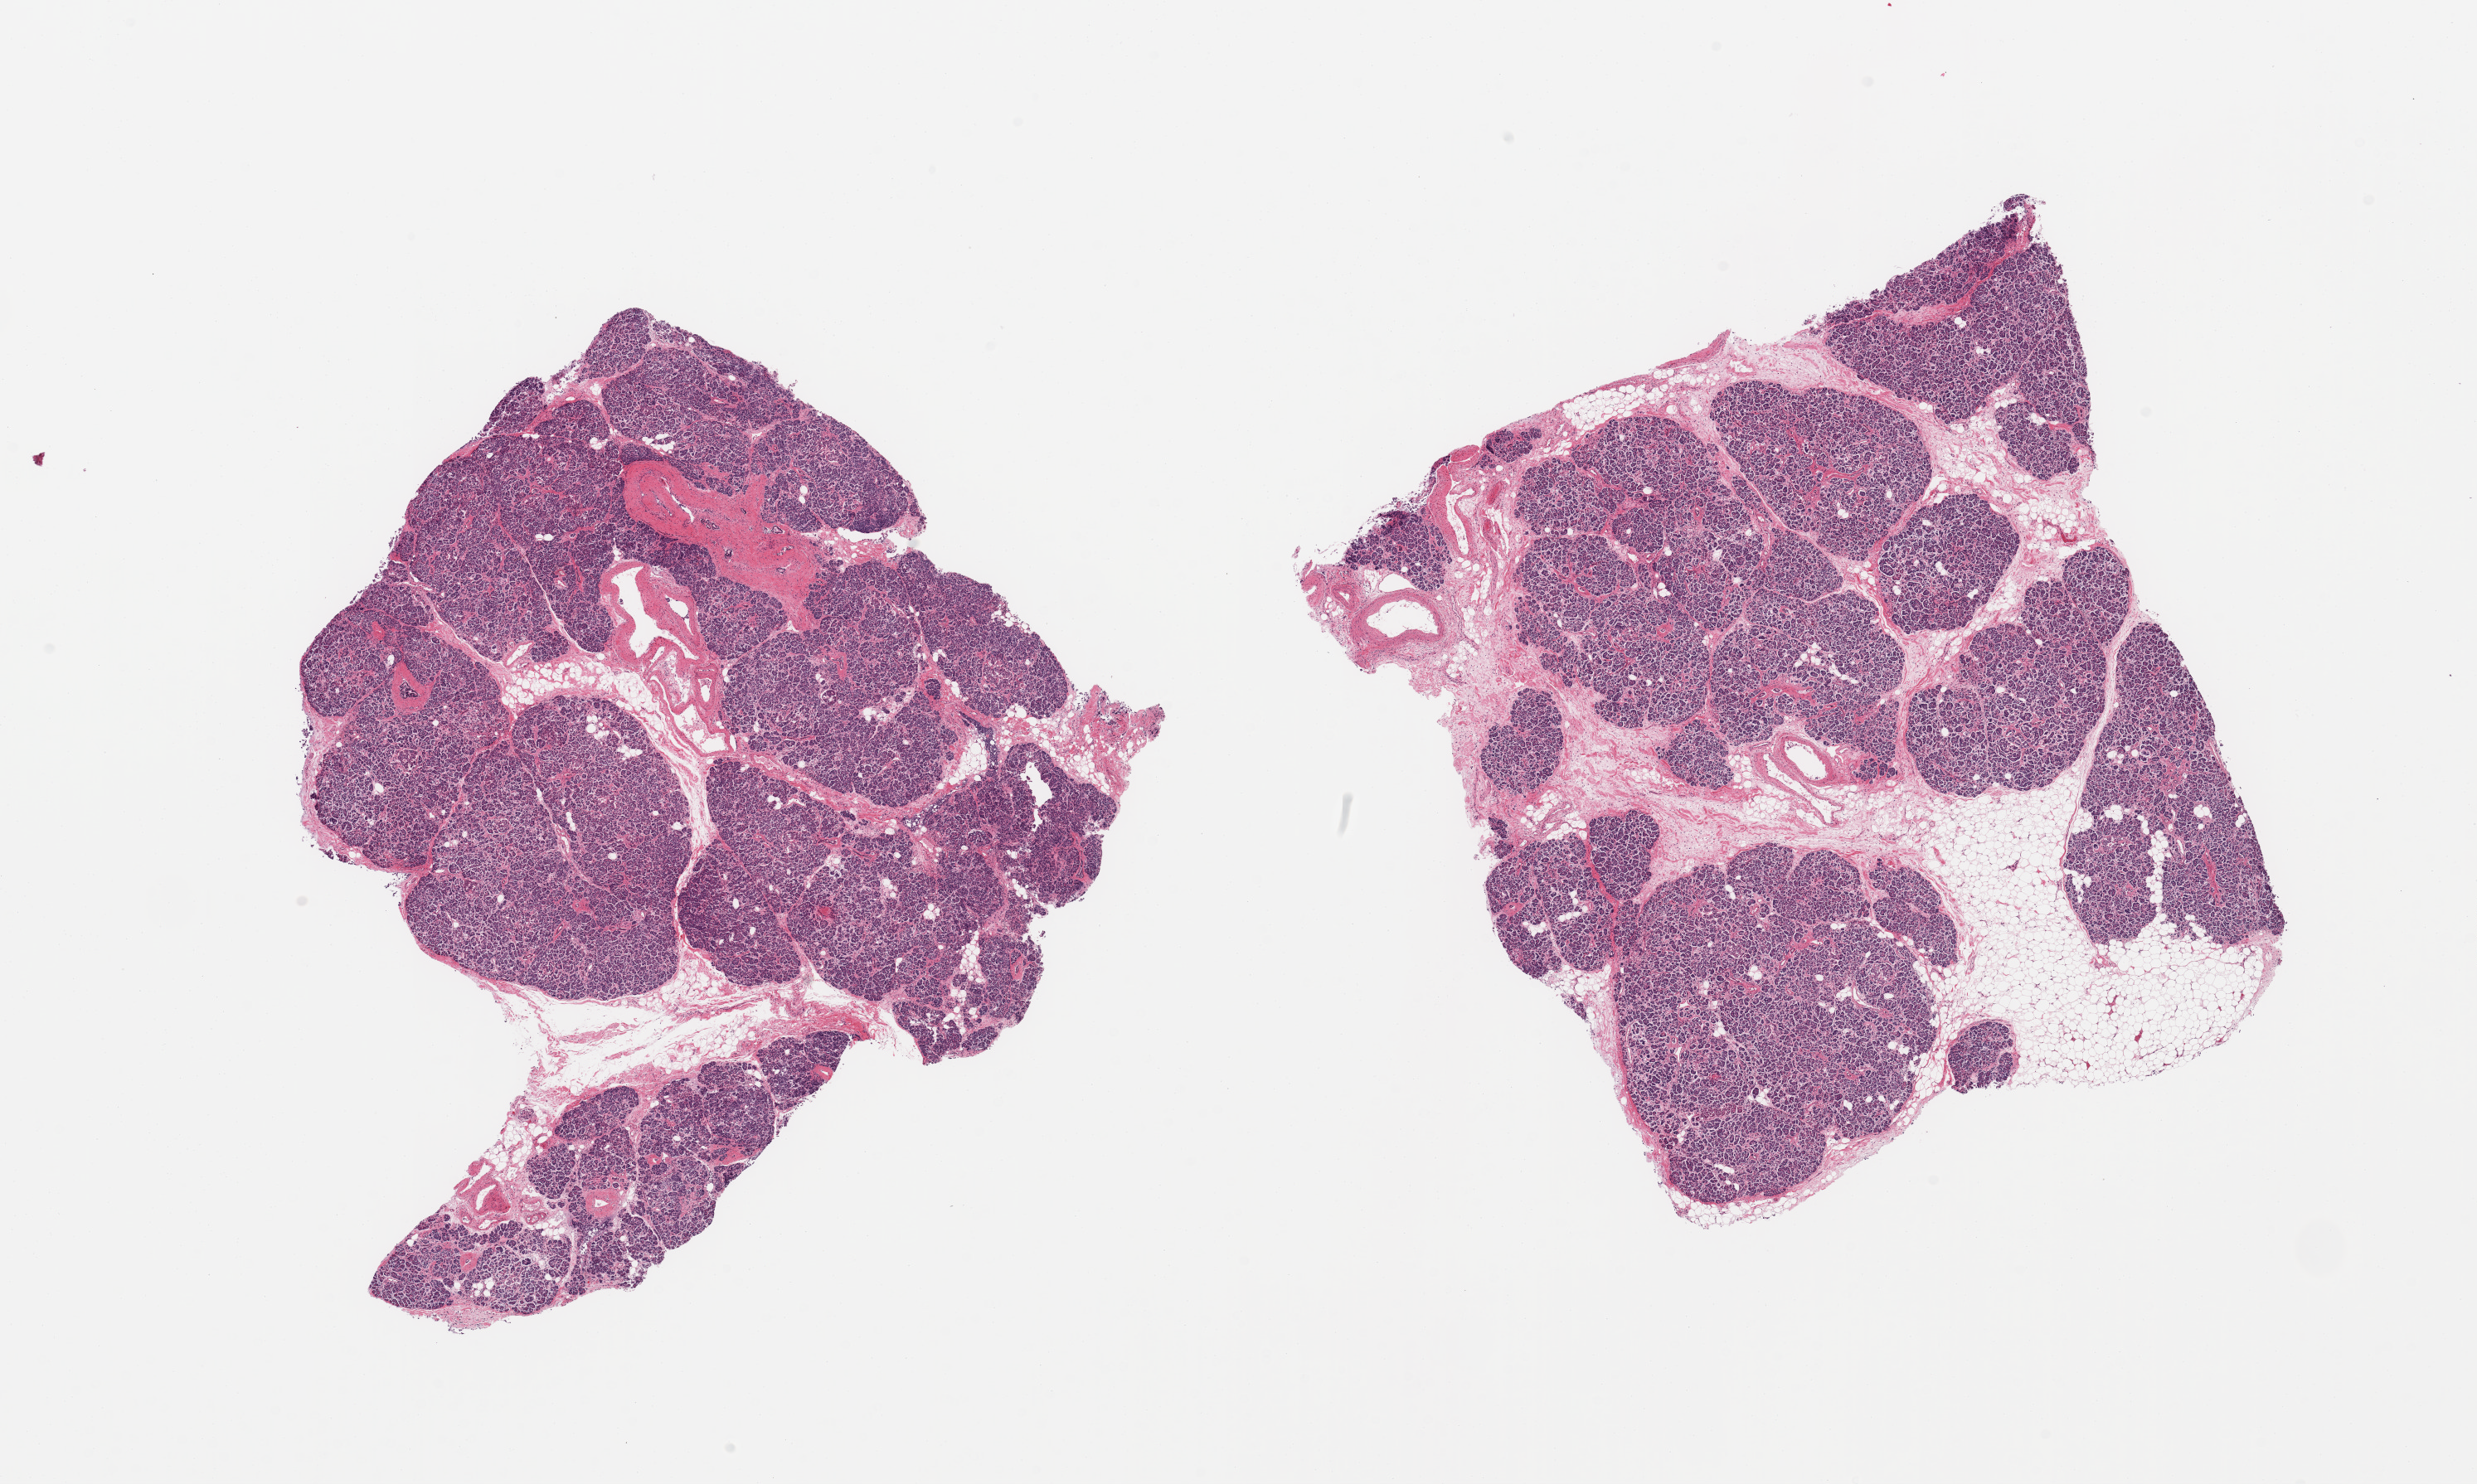
Digitized H&E-stained section, low-resolution overview of the scanned area, about 23.6 x 14.2 mm, PAXgene-fixed paraffin-embedded (PFPE) section, target tissue: pancreas, donor tissue sample. Donor sex: female.
Reviewer comment on this tissue sample: 2 pieces; 10 and 40% fat and fibrous tissue, scattered chronic inflammatory cells.